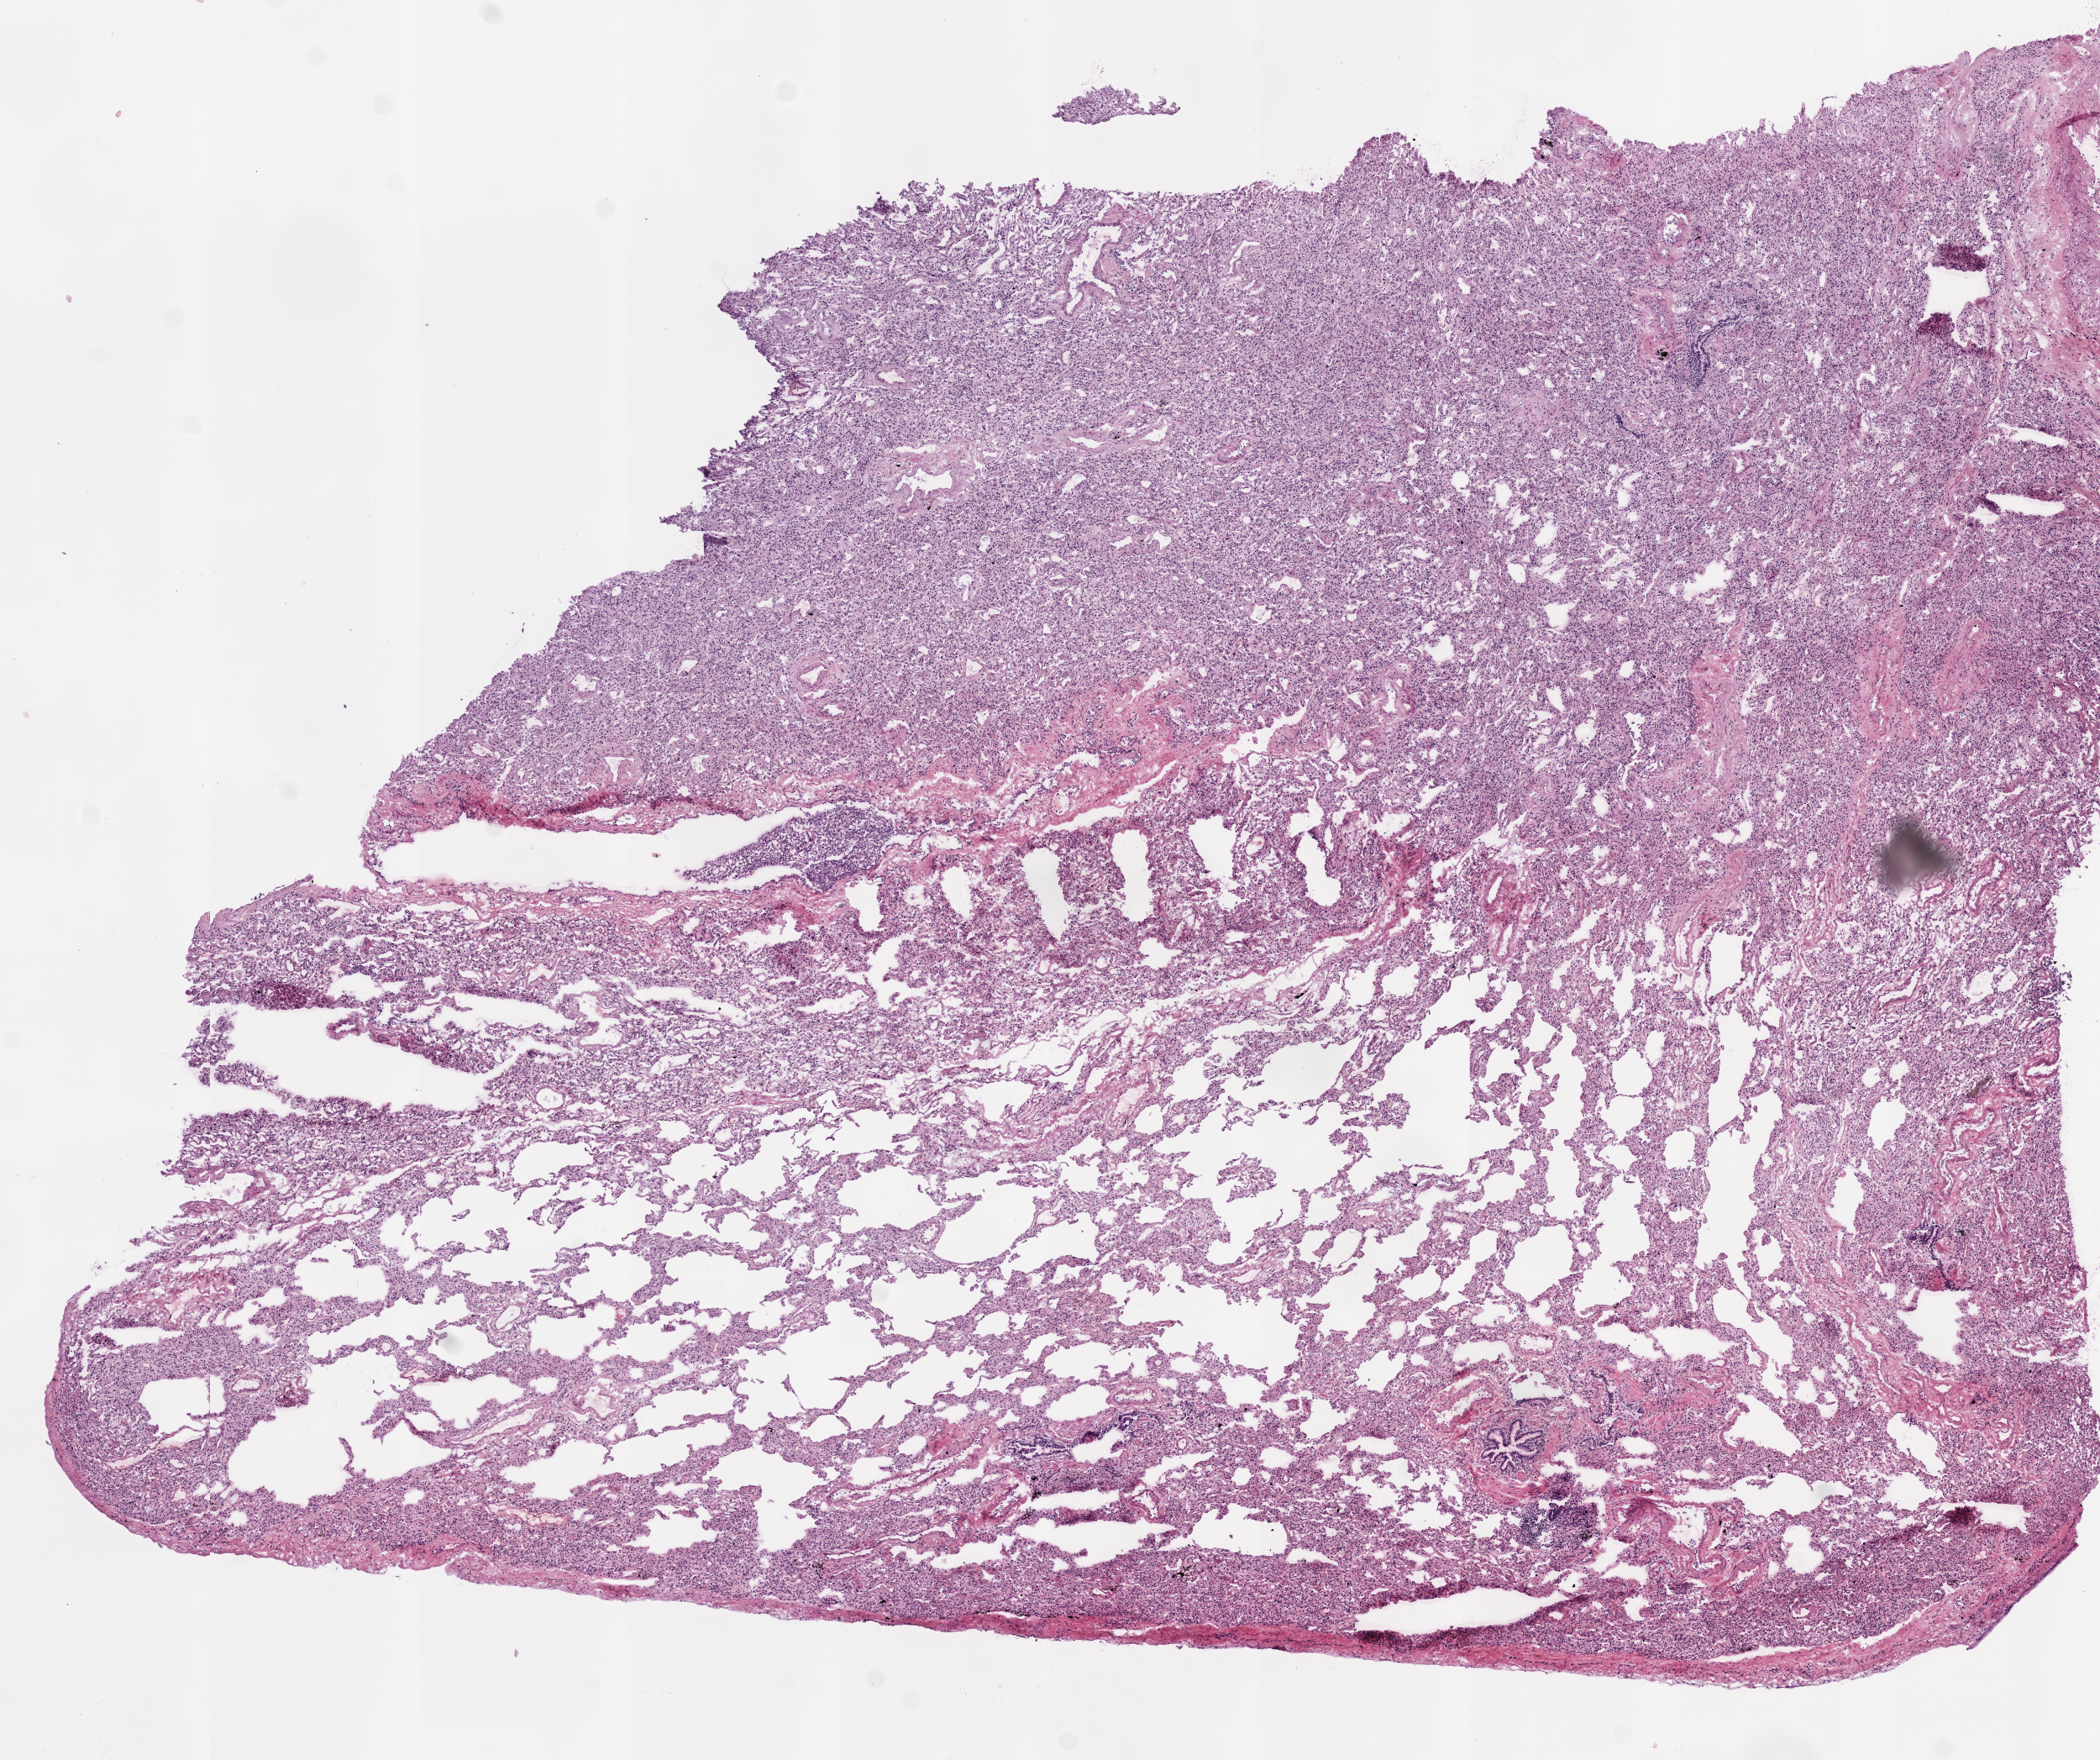
Digitized H&E tissue section (whole slide) — shown as a low-resolution overview of the whole scanned area (about 10.0 x 8.4 mm, from a 20x scan). Frozen section from the top of the tissue portion. Solid tissue normal (non-tumour tissue) sample from the lung. Patient: male, age at initial diagnosis 57 years.
This section: solid tissue normal (non-tumour) sample from the same patient. Patient diagnosis: Squamous cell carcinoma, NOS (lower lobe, lung).